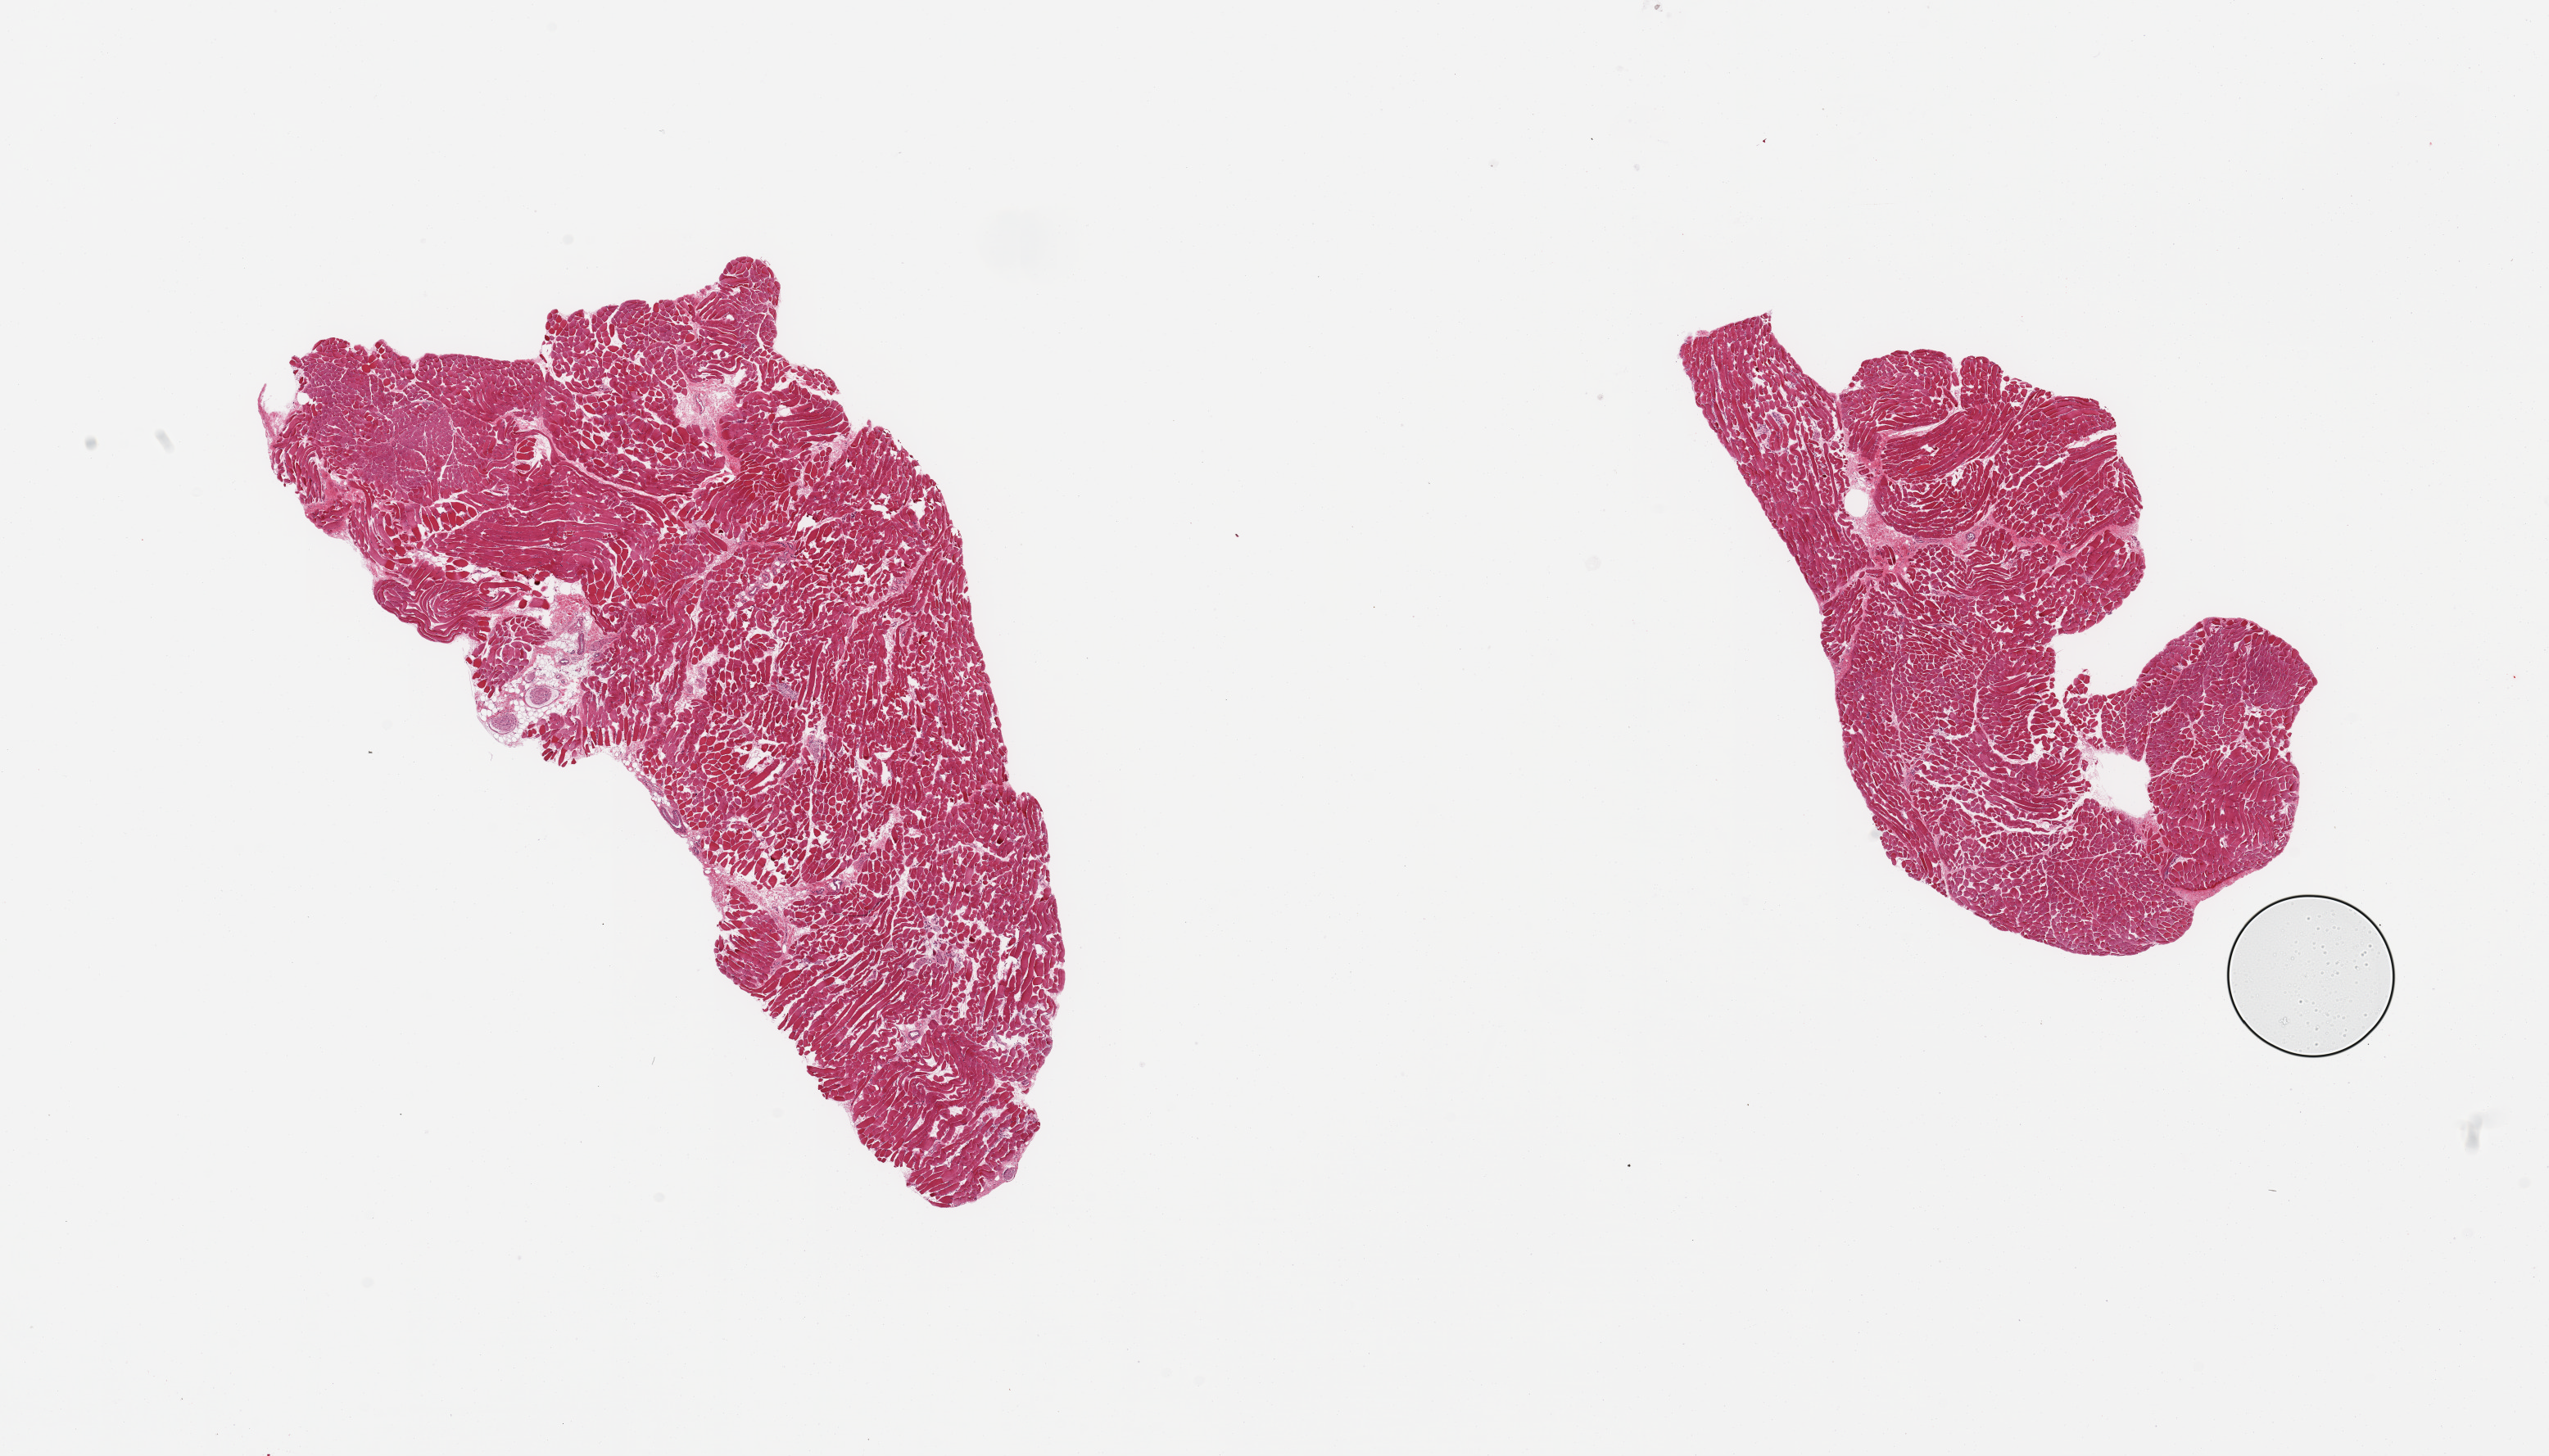
Hematoxylin and eosin (H&E) whole-slide image, low-resolution overview of the scanned area, about 24.6 x 14.1 mm (slide scanned at 20x); PAXgene-fixed paraffin-embedded (PFPE) section; section of thyroid (target tissue); tissue donor sample. Donor sex: male.
• pathologist's review note for this sample: 2 pieces; skeletal muscle not thyroid